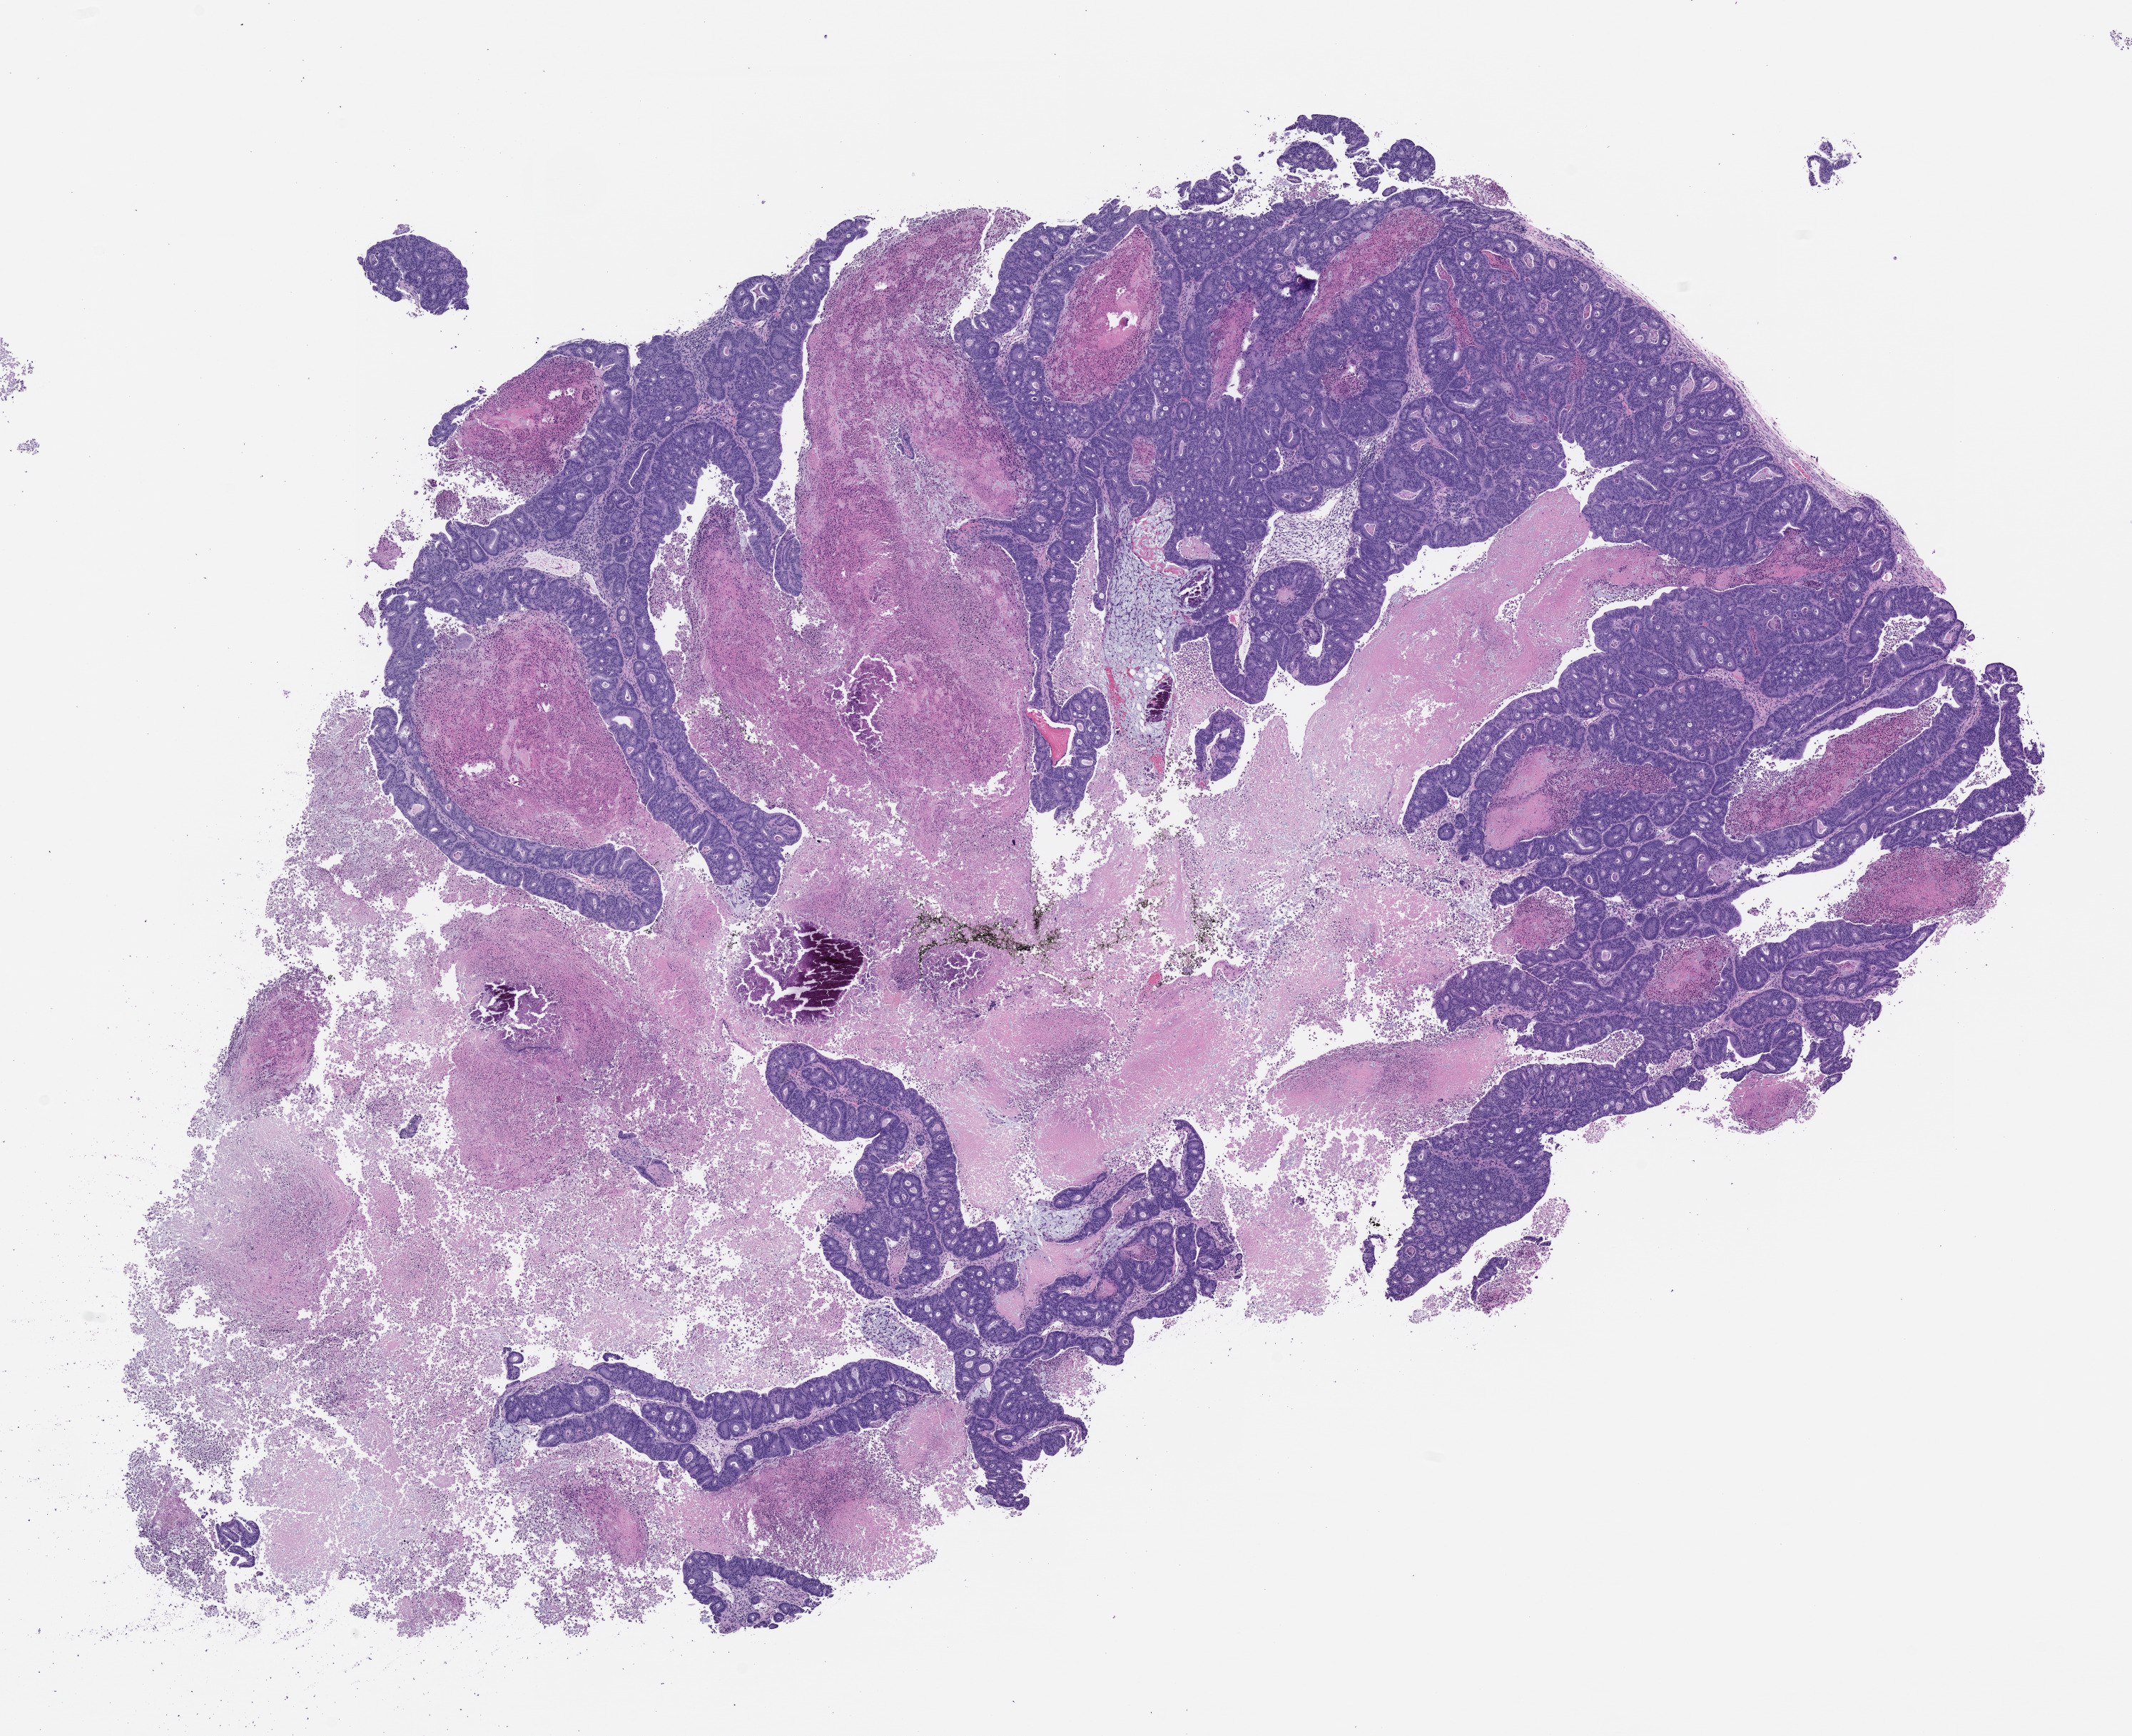
Whole-slide image, haematoxylin and eosin: patient-derived xenograft (human tumor grown in a mouse), passage 1 — shown as a low-resolution overview of the whole scanned area (about 12.0 x 9.8 mm), formalin-fixed paraffin-embedded section, originating tumor site category: rectum.
Originating patient diagnosis: Rectal Adenocarcinoma.